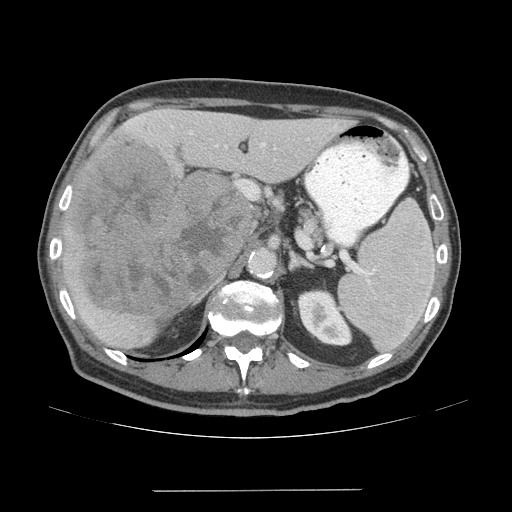
Contrast-enhanced abdominal CT (liver protocol), one axial slice. Position 35 of 77 along the scan axis. Soft-tissue window (W 400 / L 40 HU). 2.5 mm slice thickness. 512 × 512 image matrix, field of view 400 × 400 mm. From the clinical record (not read from this slice): diagnosis: hepatocellular carcinoma (patient treated with transarterial chemoembolisation; whether this scan precedes or follows treatment is not stated here); TNM stage (as recorded): Stage-IVA; Child-Pugh class: A.
Outlined on this slice (semi-automatic segmentation, software-assisted and operator-edited):
- liver parenchyma outside the tumour (the mass and vessels are separate outlines, so this box may not span the whole liver): bounding box (x1, y1, x2, y2) in pixels: (62, 108, 353, 348)
- mass: (63, 137, 255, 318)
- liver vessels: (90, 117, 336, 323)